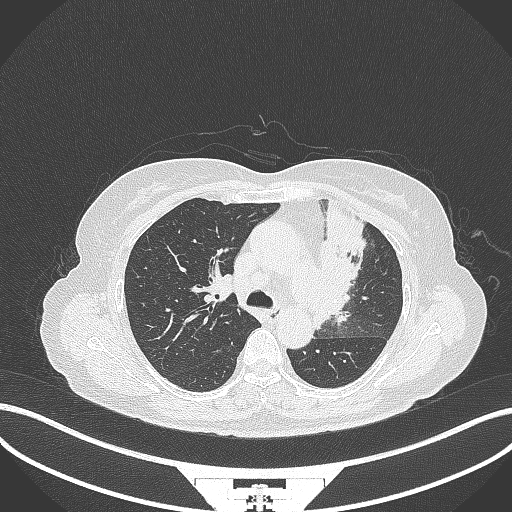
Chest CT, one axial slice; position 223 of 382 along the scan axis; reconstruction kernel B70f; lung window (W 1500 / L -600 HU); 512 × 512 image matrix, field of view 400 × 400 mm. Patient: female, 64 years. Case-level facts recorded for this patient, not image findings: clinical TNM (as recorded): T2a N2 M0.
Structures marked on this image (rectangle marked by the reading radiologist):
- lung tumour (recorded histology: adenocarcinoma): bounding box [x1, y1, x2, y2] px = [310, 196, 369, 335]